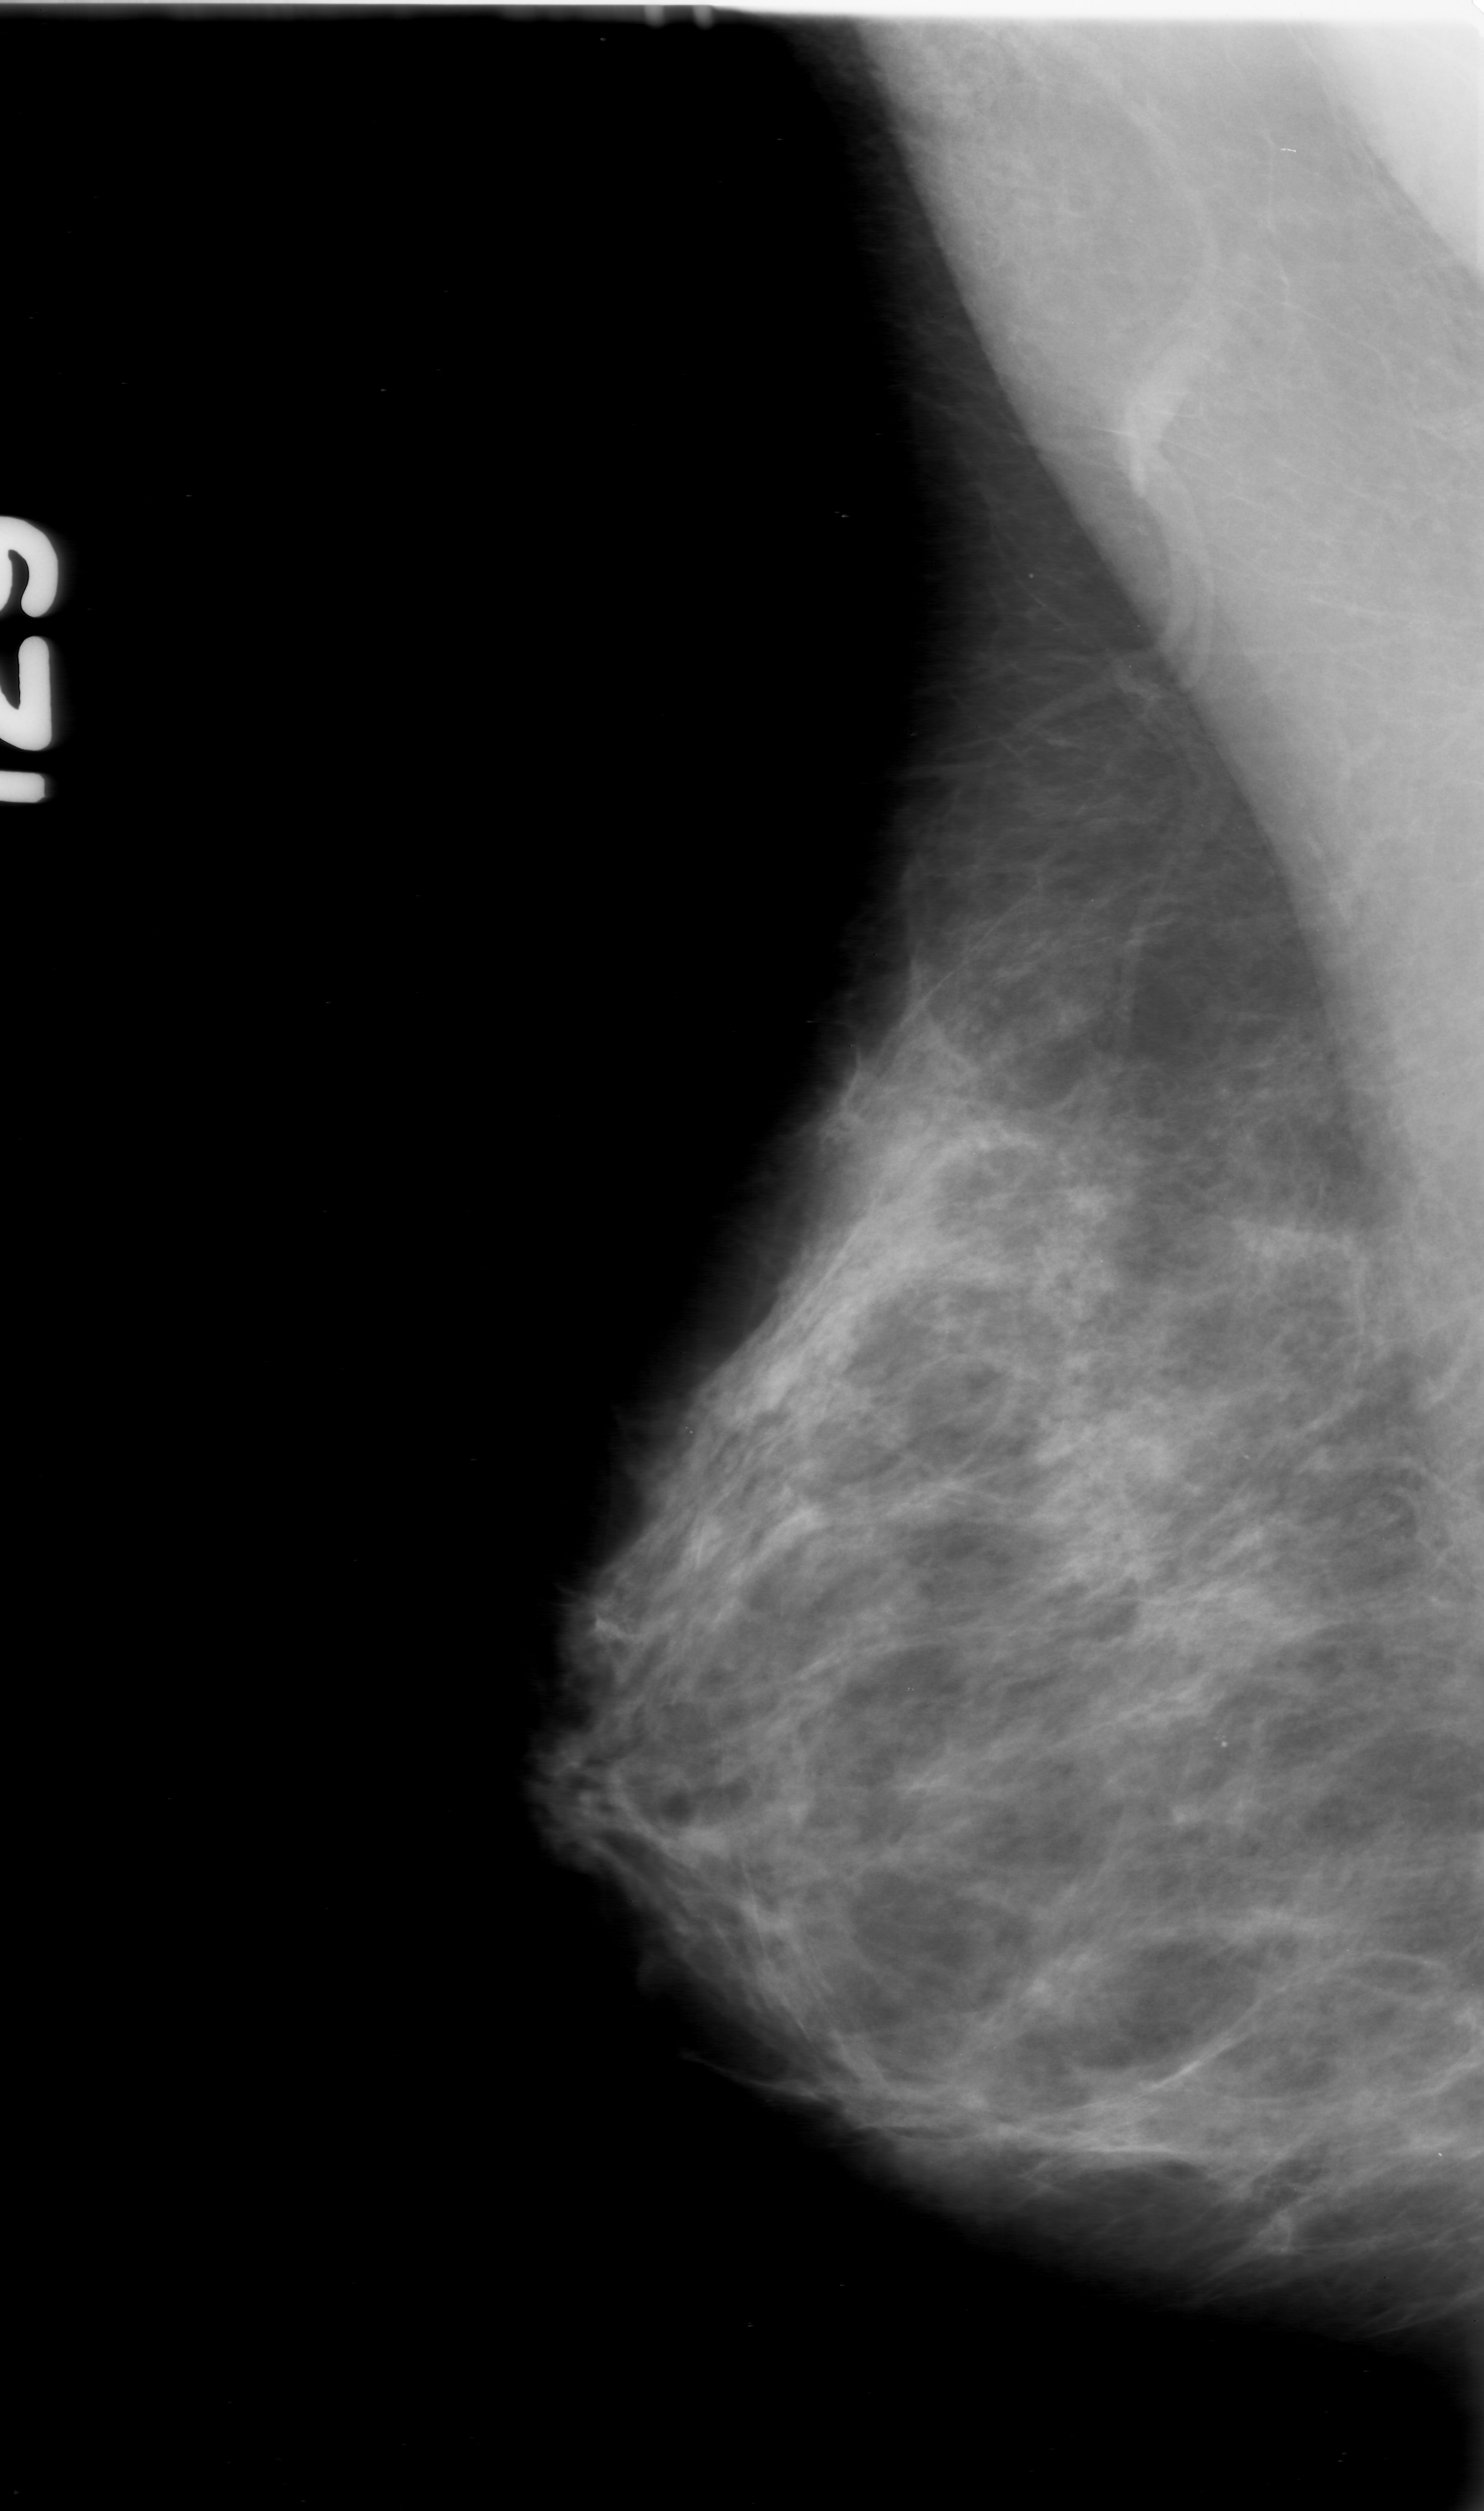
Scanned film-screen mammogram, right breast, mediolateral oblique (MLO) view, breast composition: heterogeneously dense (BI-RADS density category 3 of 4).
Finding: calcifications, morphology punctate, distribution clustered; BI-RADS assessment category 0; pathology result (as recorded, not read from the image): malignant.